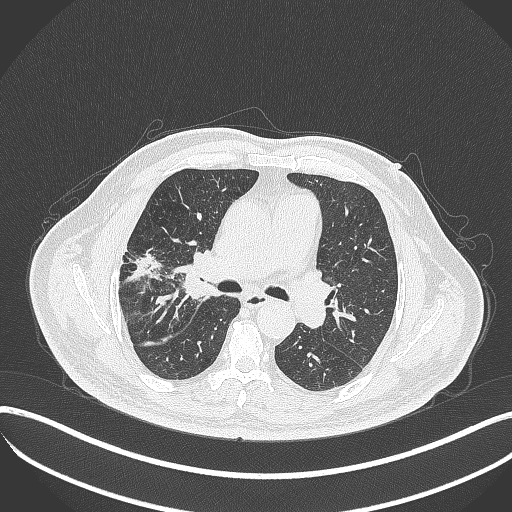
Chest CT, one axial slice; reconstruction kernel B70f; 120 kVp; lung window (W 1500 / L -600 HU); 1 mm slice thickness; 512 × 512 image matrix. Patient: male, 72 years. Case-level facts recorded for this patient, not image findings: clinical TNM (as recorded): T1c N0 M0.
Outlined on this slice (bounding box drawn by a radiologist):
- lung tumour (recorded histology: squamous cell carcinoma): bounding box <173,233,205,309> (left, top, right, bottom; pixels)